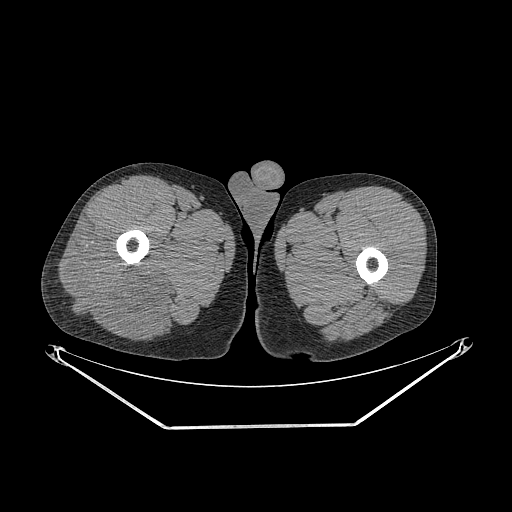
CT of an extremity soft-tissue mass (from a PET/CT study), one axial slice; position 263 of 267 along the scan axis; reconstruction kernel STANDARD; soft-tissue window (W 400 / L 40 HU); 3.75 mm slice thickness; 512 × 512 image matrix. Male patient. Case-level facts recorded for this patient, not image findings: histological type: poorly differentiated synovial sarcoma; grade: high; site of the primary tumour: right buttock.
Outlined on this slice (expert contour drawn on MRI and transferred to this co-registered scan by the dataset authors):
- gross tumour volume including surrounding oedema: bounding box [x1, y1, x2, y2] px = [57, 224, 177, 334]
- gross tumour volume (mass): [59, 224, 165, 334]